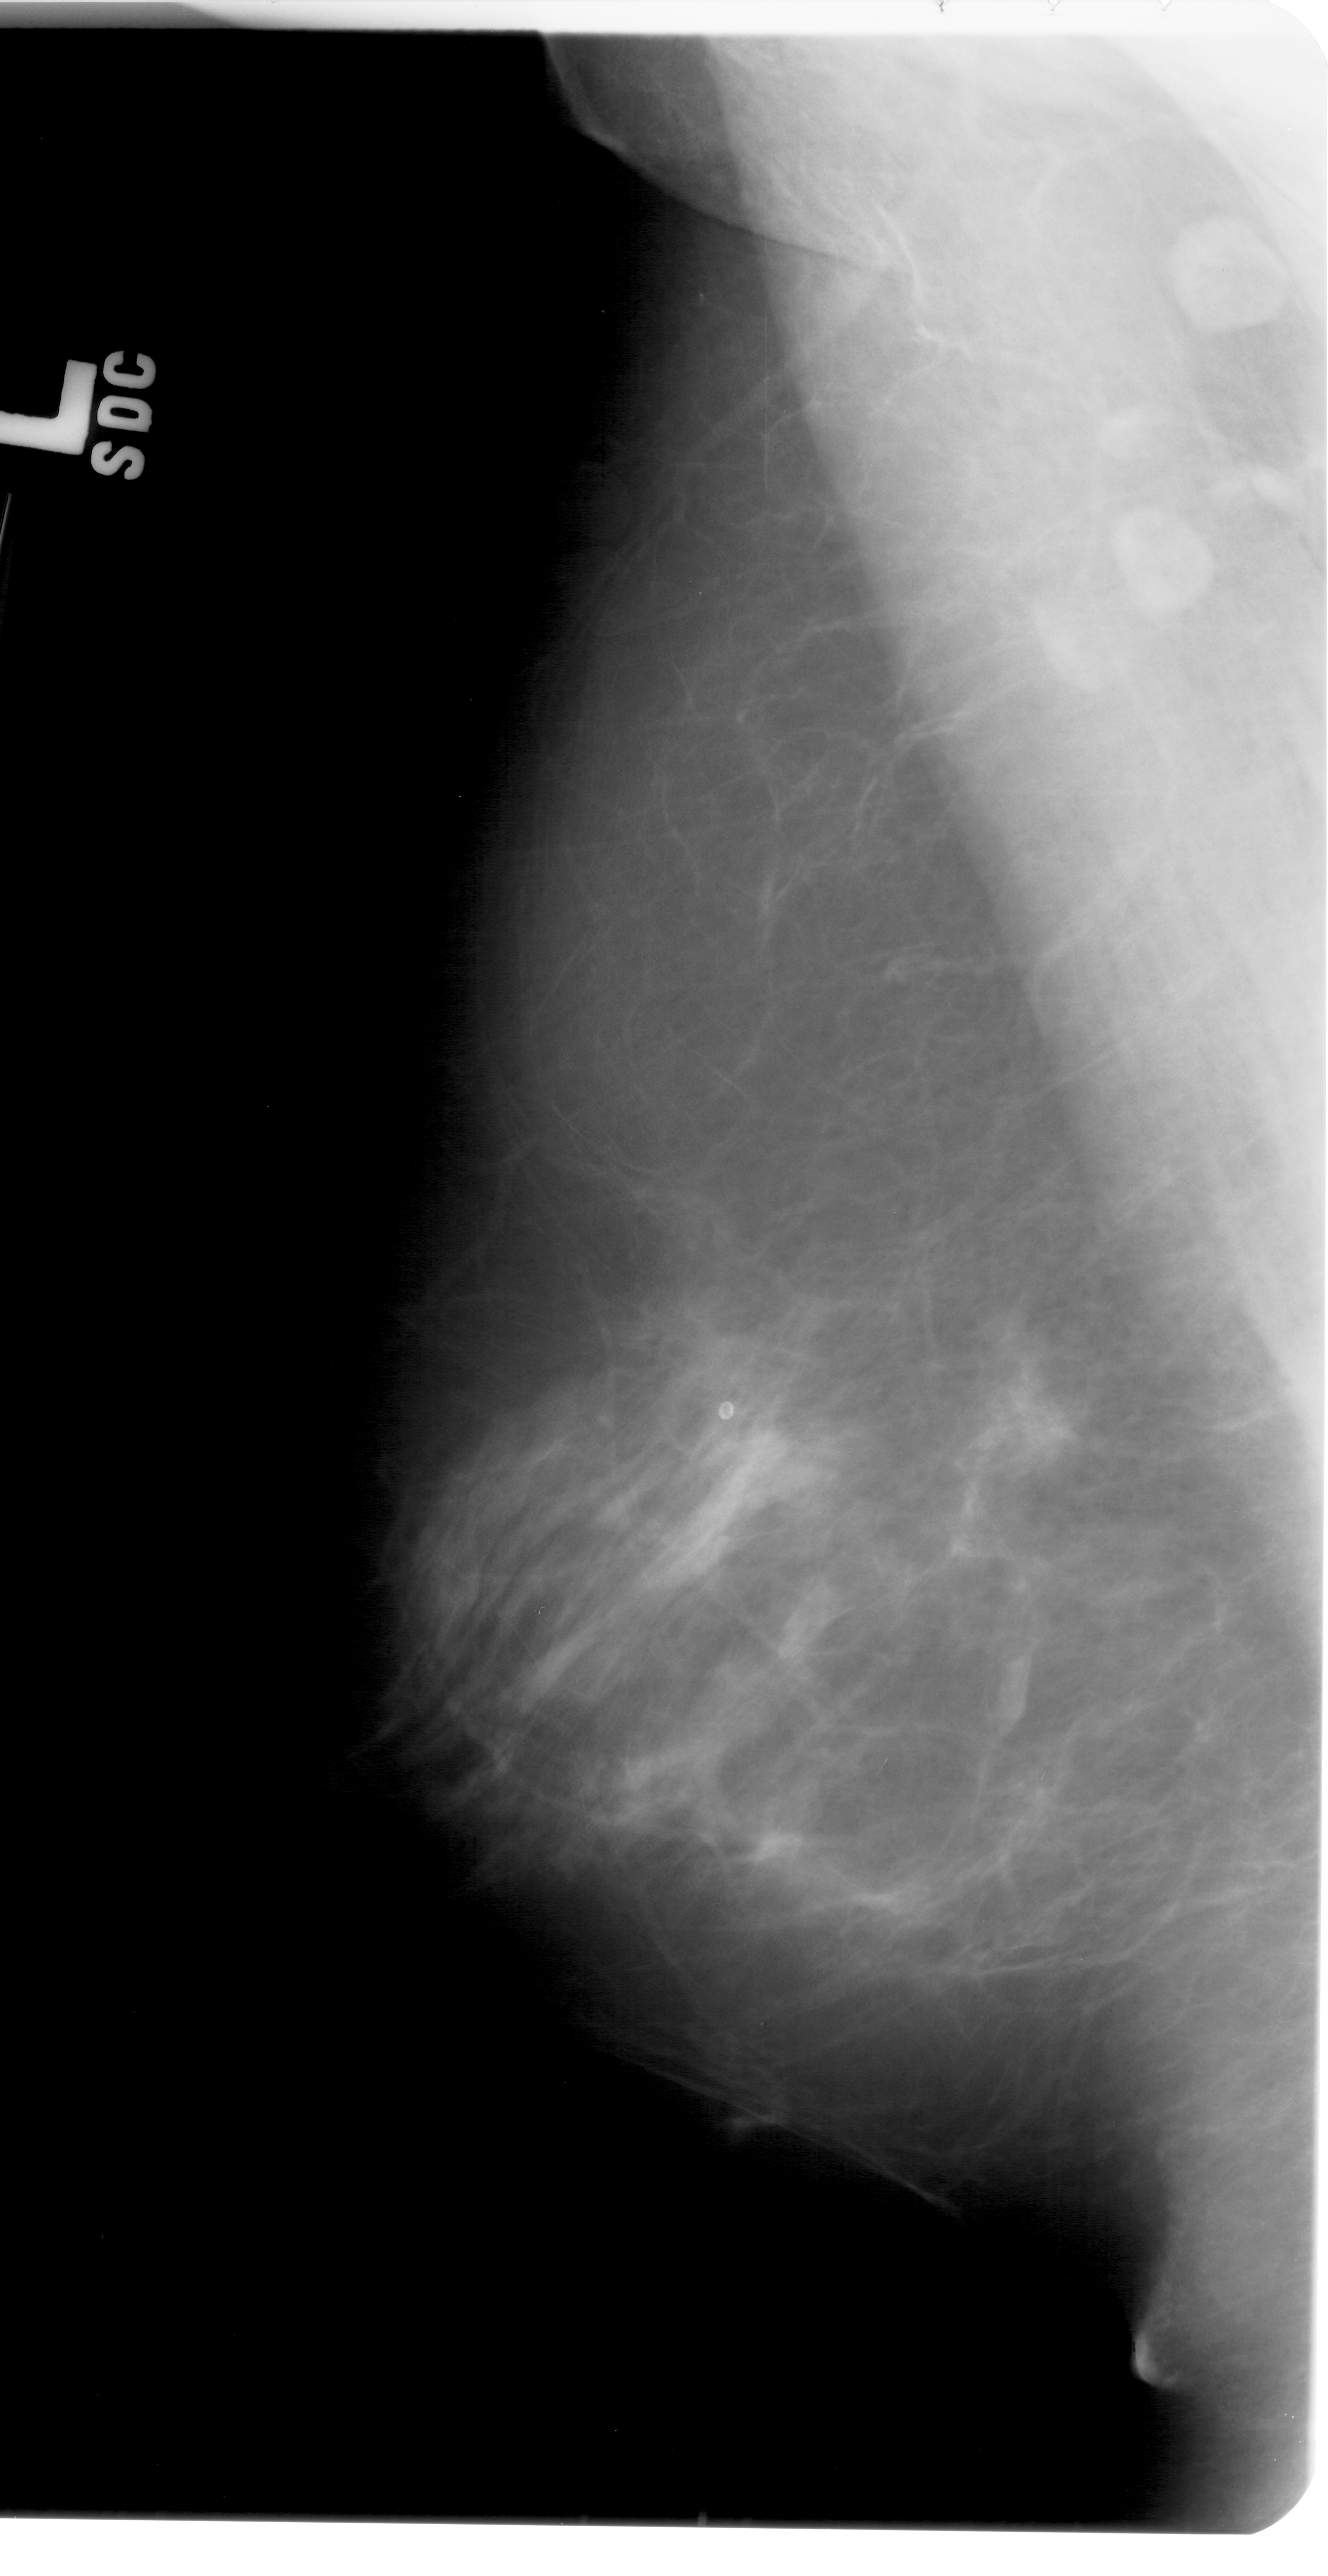
Scanned film-screen mammogram, left breast, MLO view.
- Marked abnormality: mass, shape irregular, margins ill defined; BI-RADS assessment category 4; pathology (as recorded): benign.